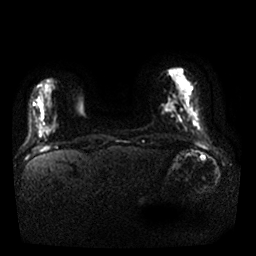
Breast MRI, one axial slice. Position 4 of 25 along the scan axis. Diffusion-weighted series; image 2 of 4 stored at this slice position (different b-values; order by instance number). 1.5 T. 4 mm slice thickness. 256 × 256 image matrix, field of view 340 × 340 mm. Female patient.
Outlined on this slice (manually delineated by an expert):
- tumour on diffusion-weighted imaging: box from (x=164, y=103) to (x=174, y=111) px